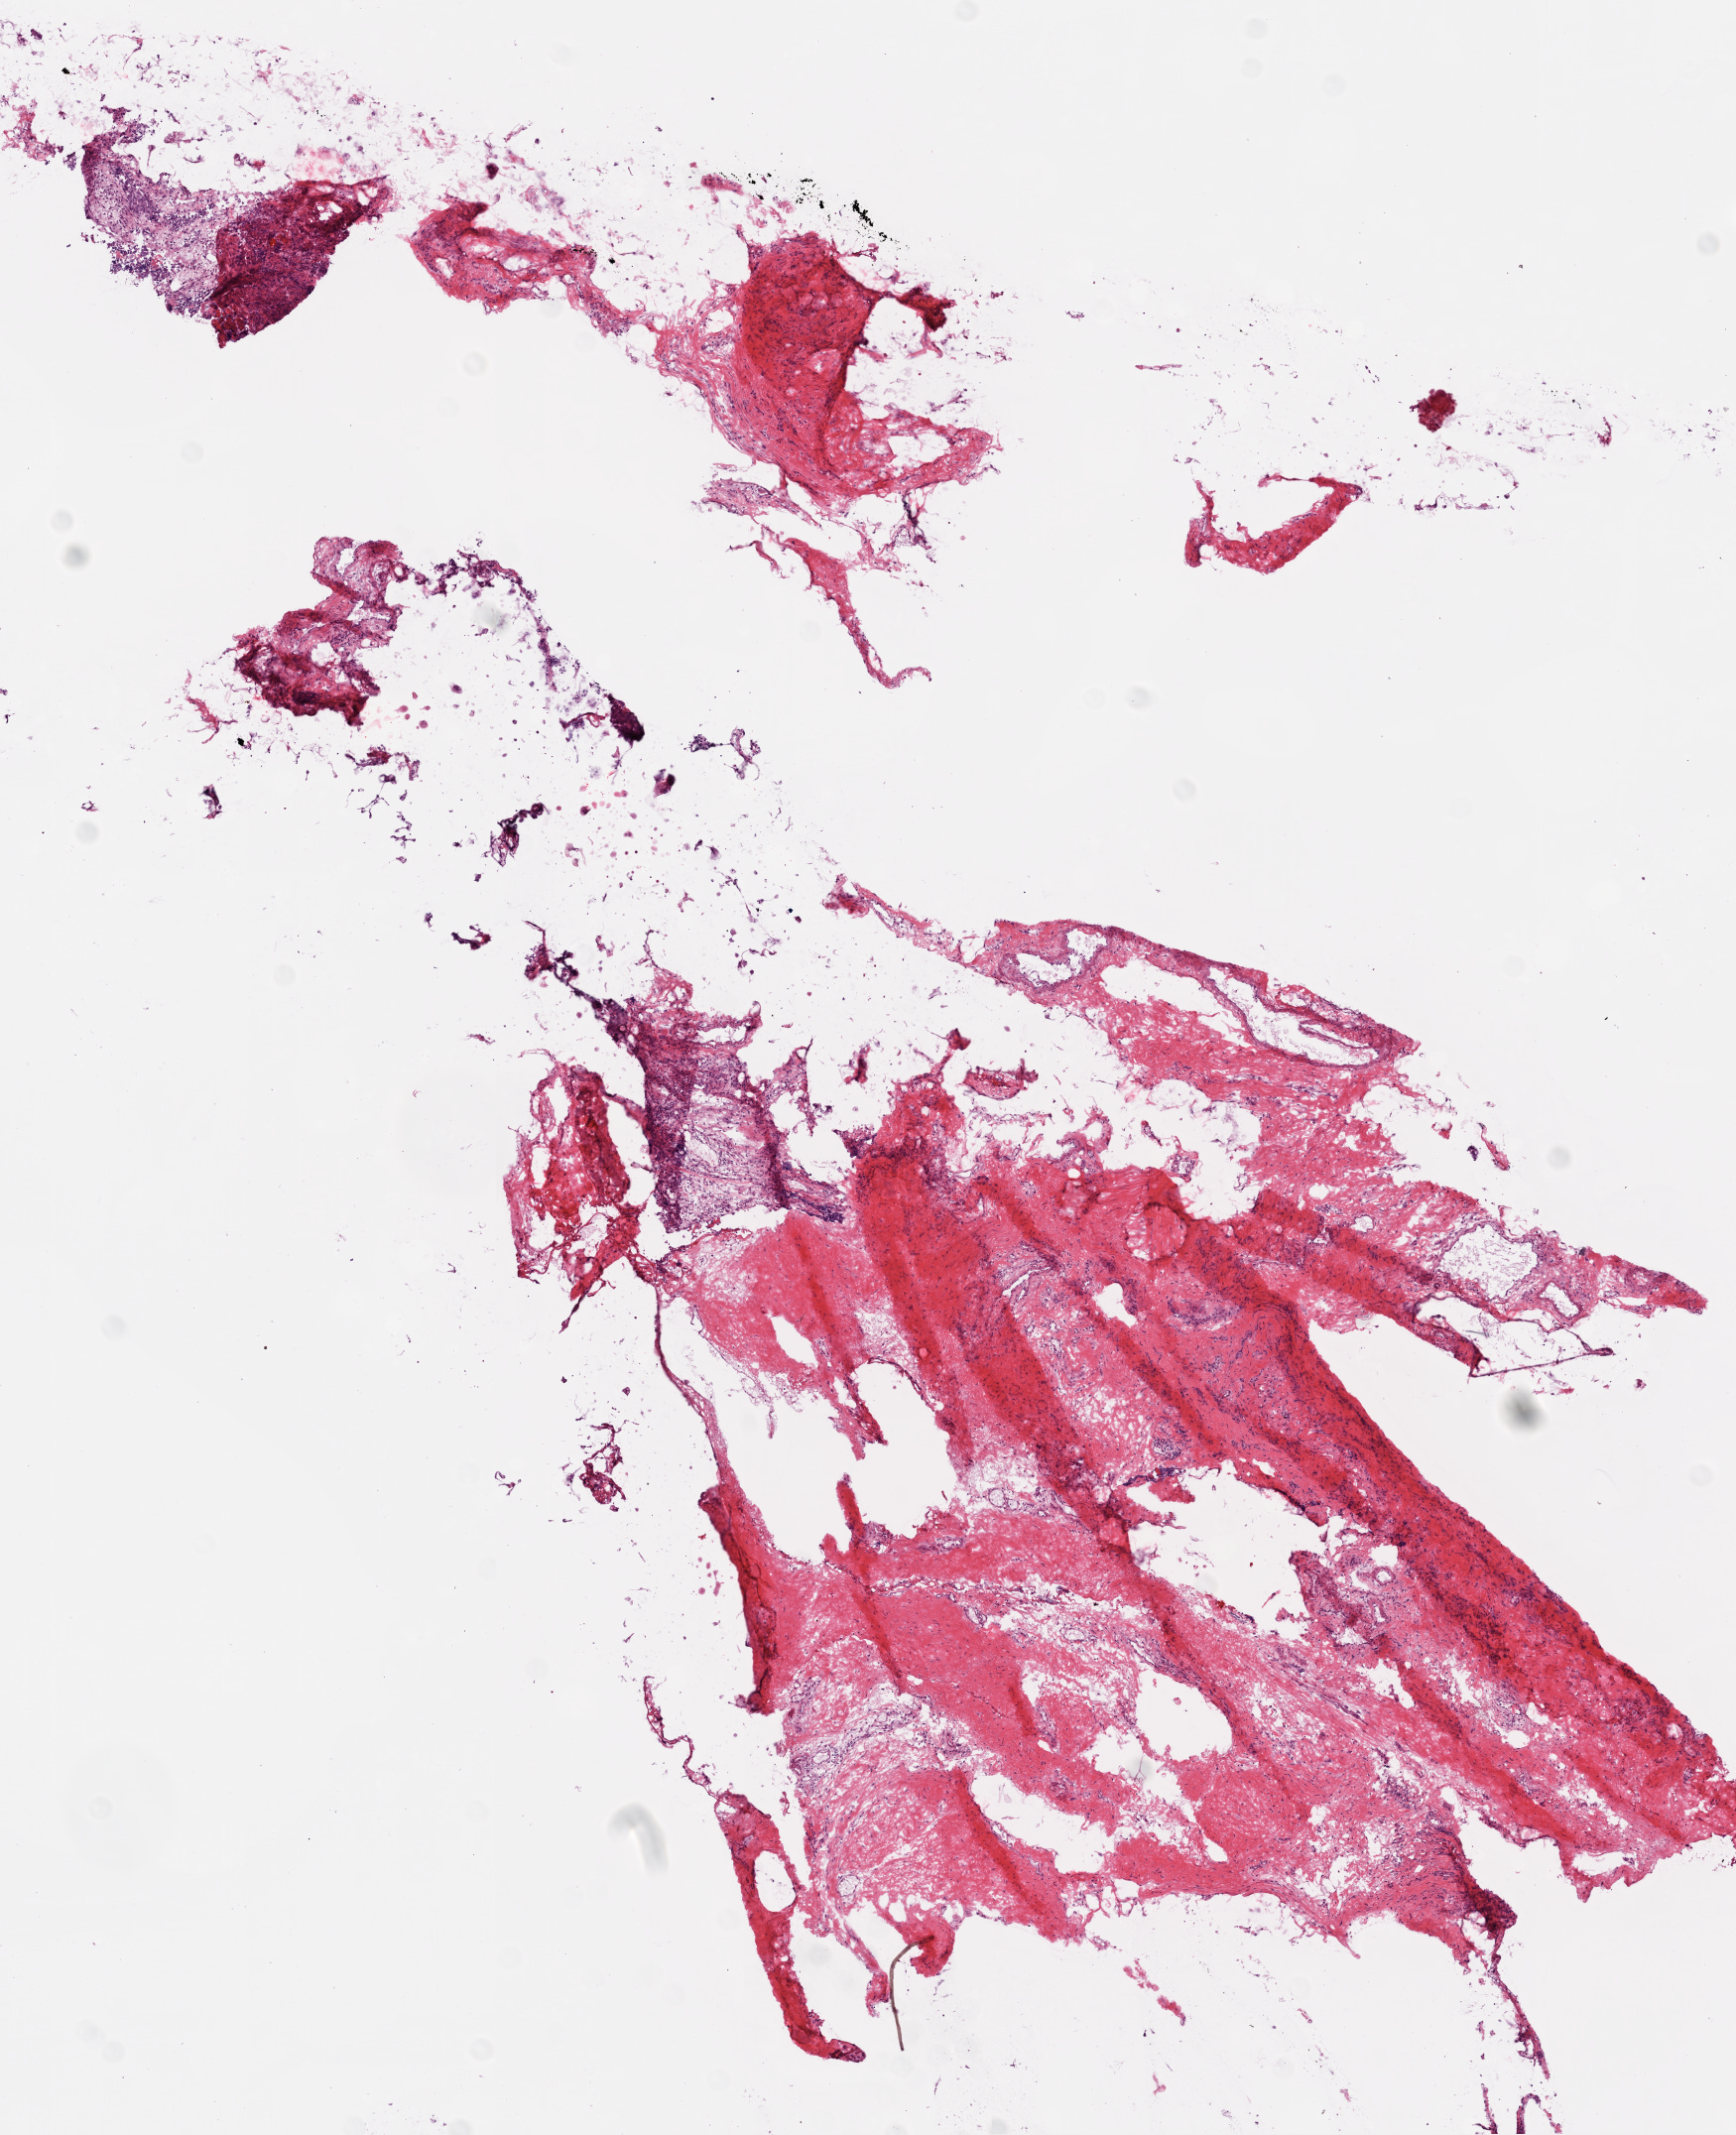
Digitized Hematoxylin and eosin (H&E) stained tissue section (whole slide) — shown as a low-resolution overview of the whole scanned area (about 7.0 x 8.6 mm, from a 20x scan); frozen section from the top of the tissue portion; ovary, solid tissue normal (non-tumour tissue) sample. Female, age 57 years at initial diagnosis.
• this section: solid tissue normal (non-tumour) sample from the same patient
• patient diagnosis: Serous cystadenocarcinoma, NOS